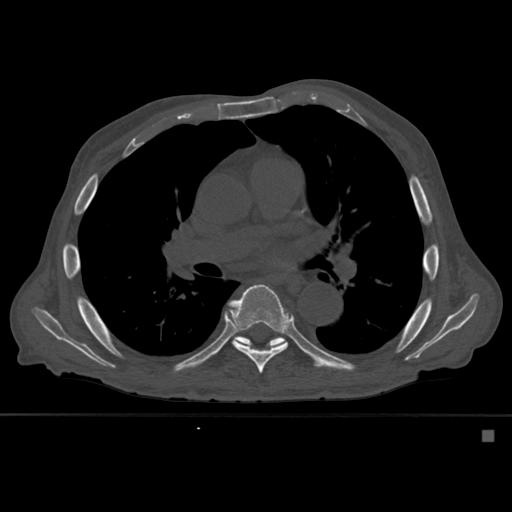
CT including the spine, one axial slice. Position 364 of 527 along the scan axis. Bone window (W 1800 / L 400 HU). 1.5 mm slice thickness. 512 × 512 image matrix, field of view 373 × 373 mm. Male patient, age 78 years. From the clinical record (not read from this slice): primary cancer: prostate.
Structures marked on this image (semi-automatically segmented with operator editing):
- T7 vertebra: bounding box <228,284,293,374> (left, top, right, bottom; pixels)
- T8 vertebra: <237,336,285,347>